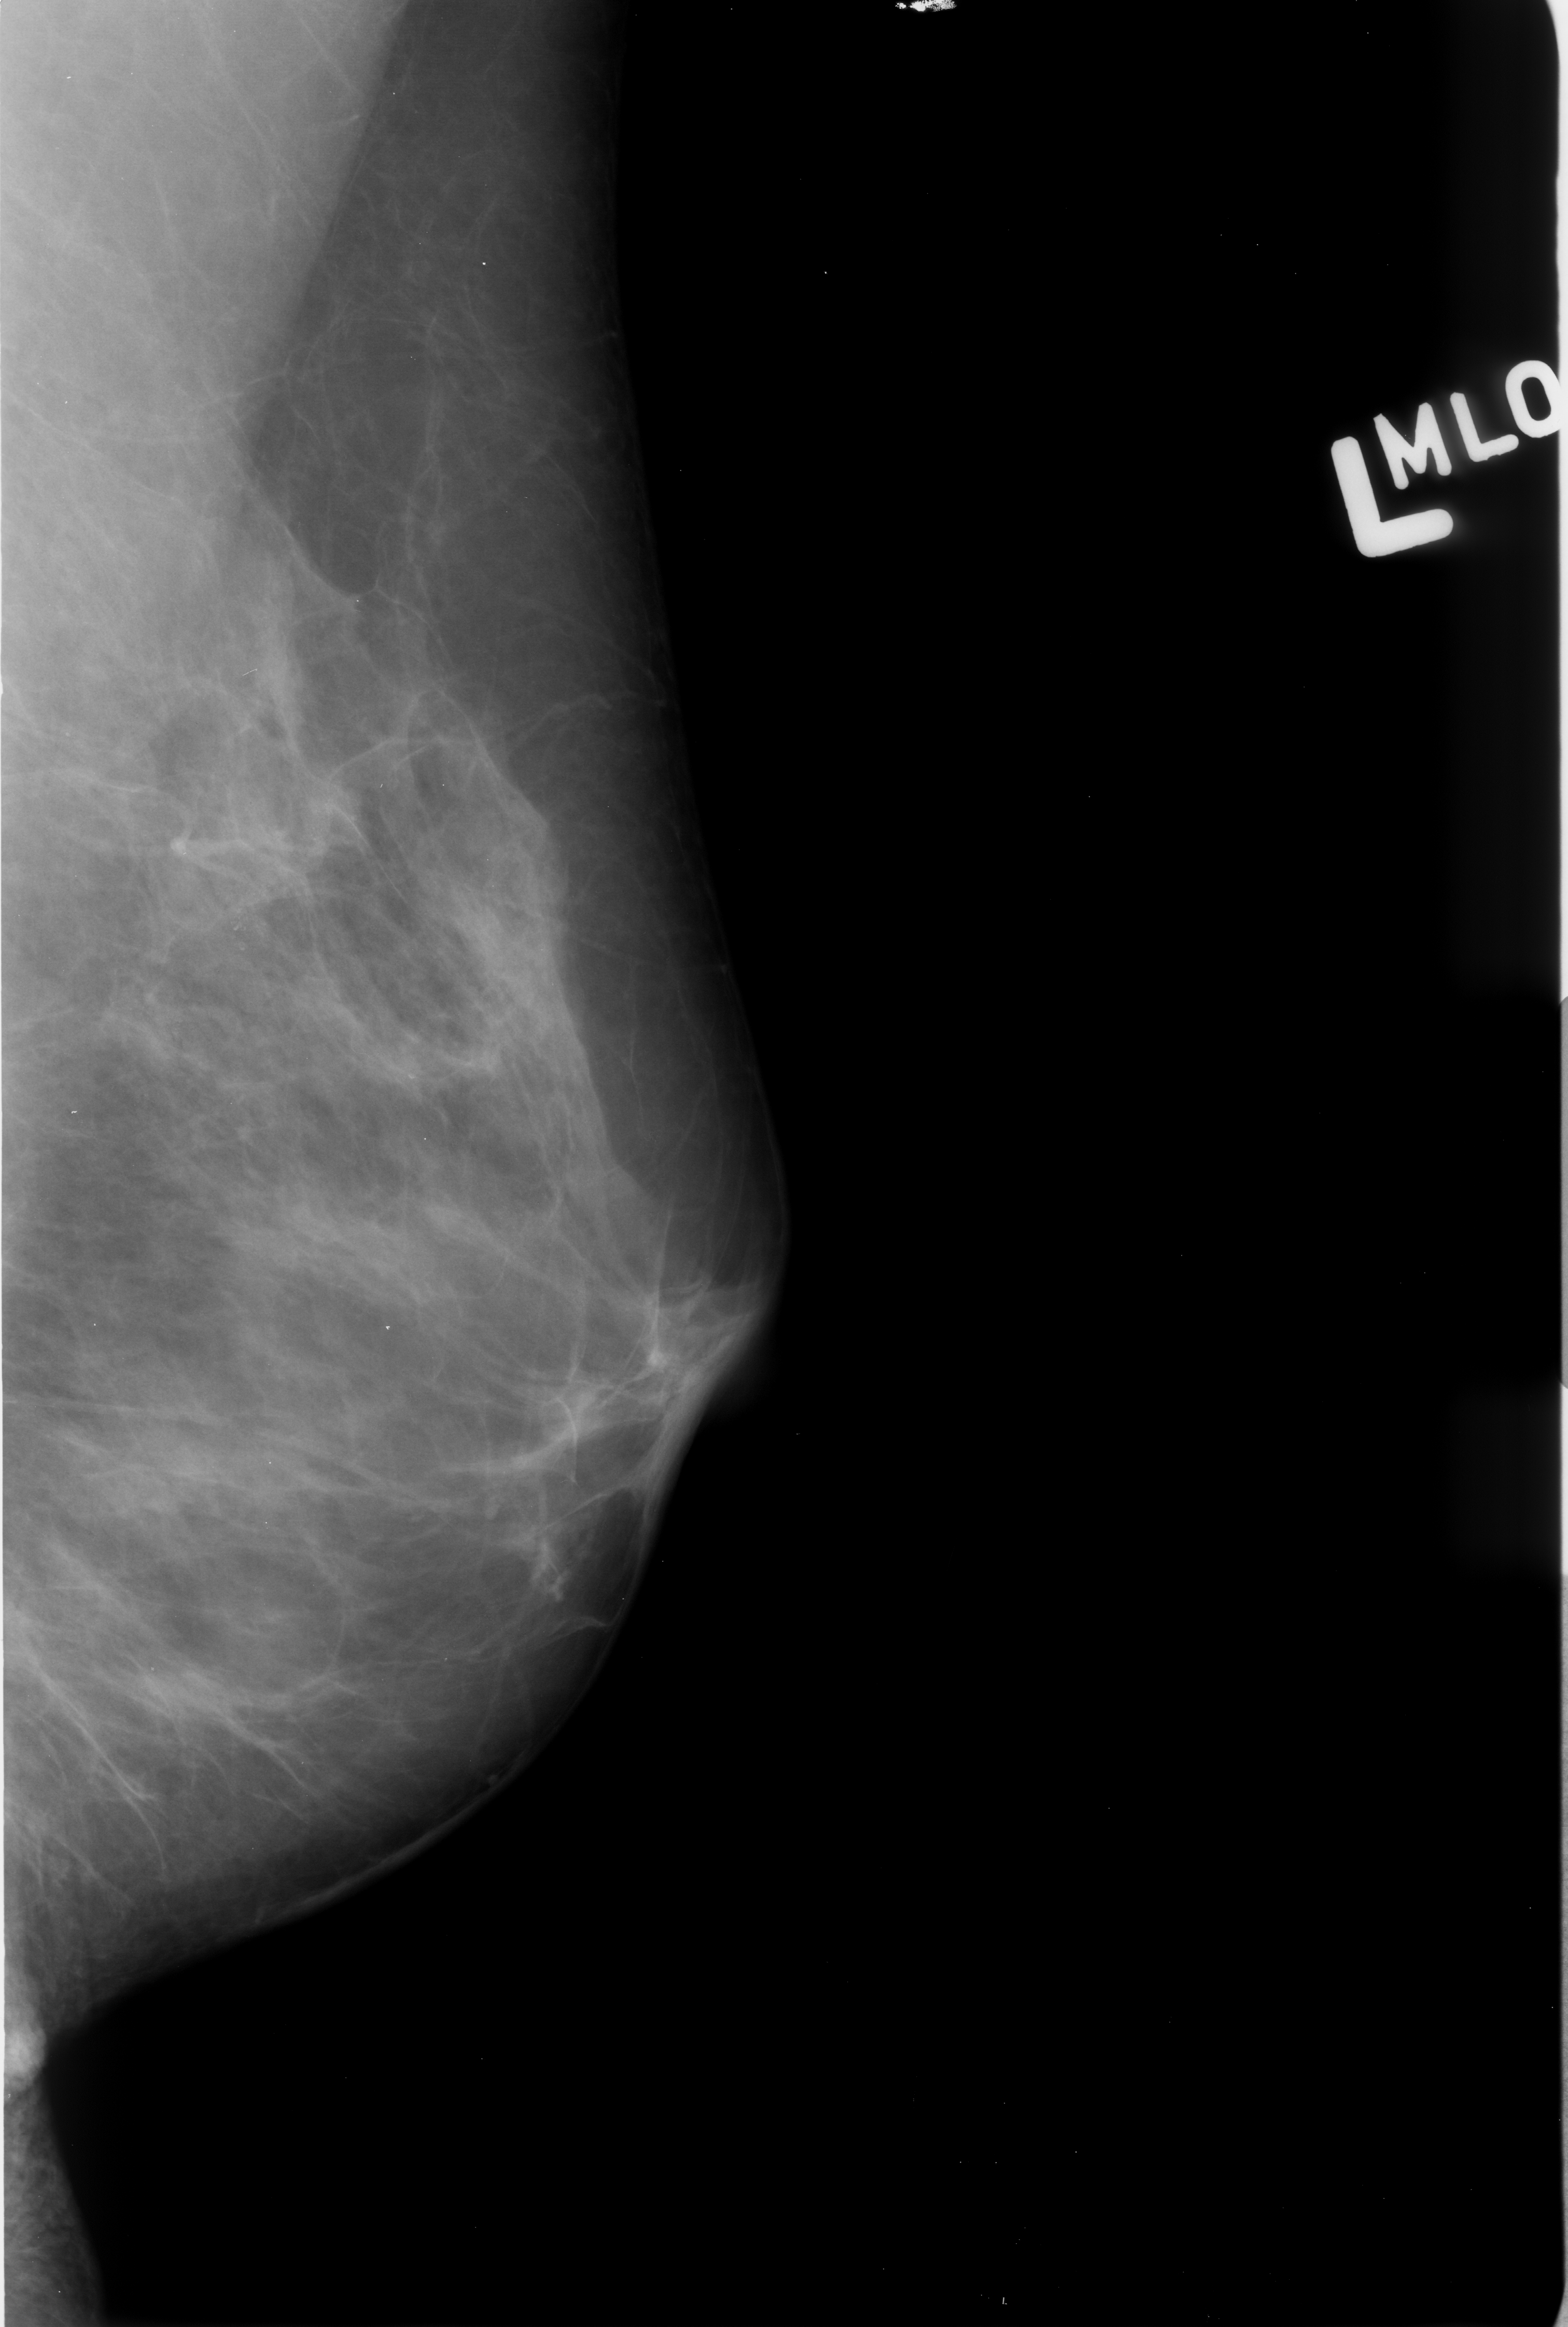
Scanned film-screen mammogram; left breast; mediolateral oblique (MLO) view; breast composition: scattered fibroglandular densities (BI-RADS density category 2 of 4).
Radiologist-marked abnormalities on this image: calcifications, morphology pleomorphic, distribution clustered; BI-RADS assessment category 4; pathology result (as recorded, not read from the image): benign.